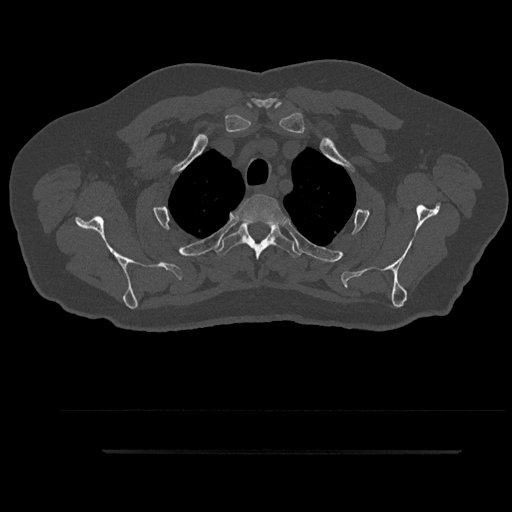
CT including the spine, one axial slice; position 733 of 797 along the scan axis; reconstruction kernel Br40s/3; bone window (W 1800 / L 400 HU); 512 × 512 image matrix, field of view 432 × 432 mm. Patient: male, 63 years. Case-level facts recorded for this patient, not image findings: primary cancer: renal; vertebrae with lytic lesions (as recorded): T8.
Annotated regions visible in this slice (semi-automatic segmentation, software-assisted and operator-edited):
- T2 vertebra: box from (x=236, y=194) to (x=285, y=241) px
- T3 vertebra: (x=215, y=222)–(x=302, y=260)